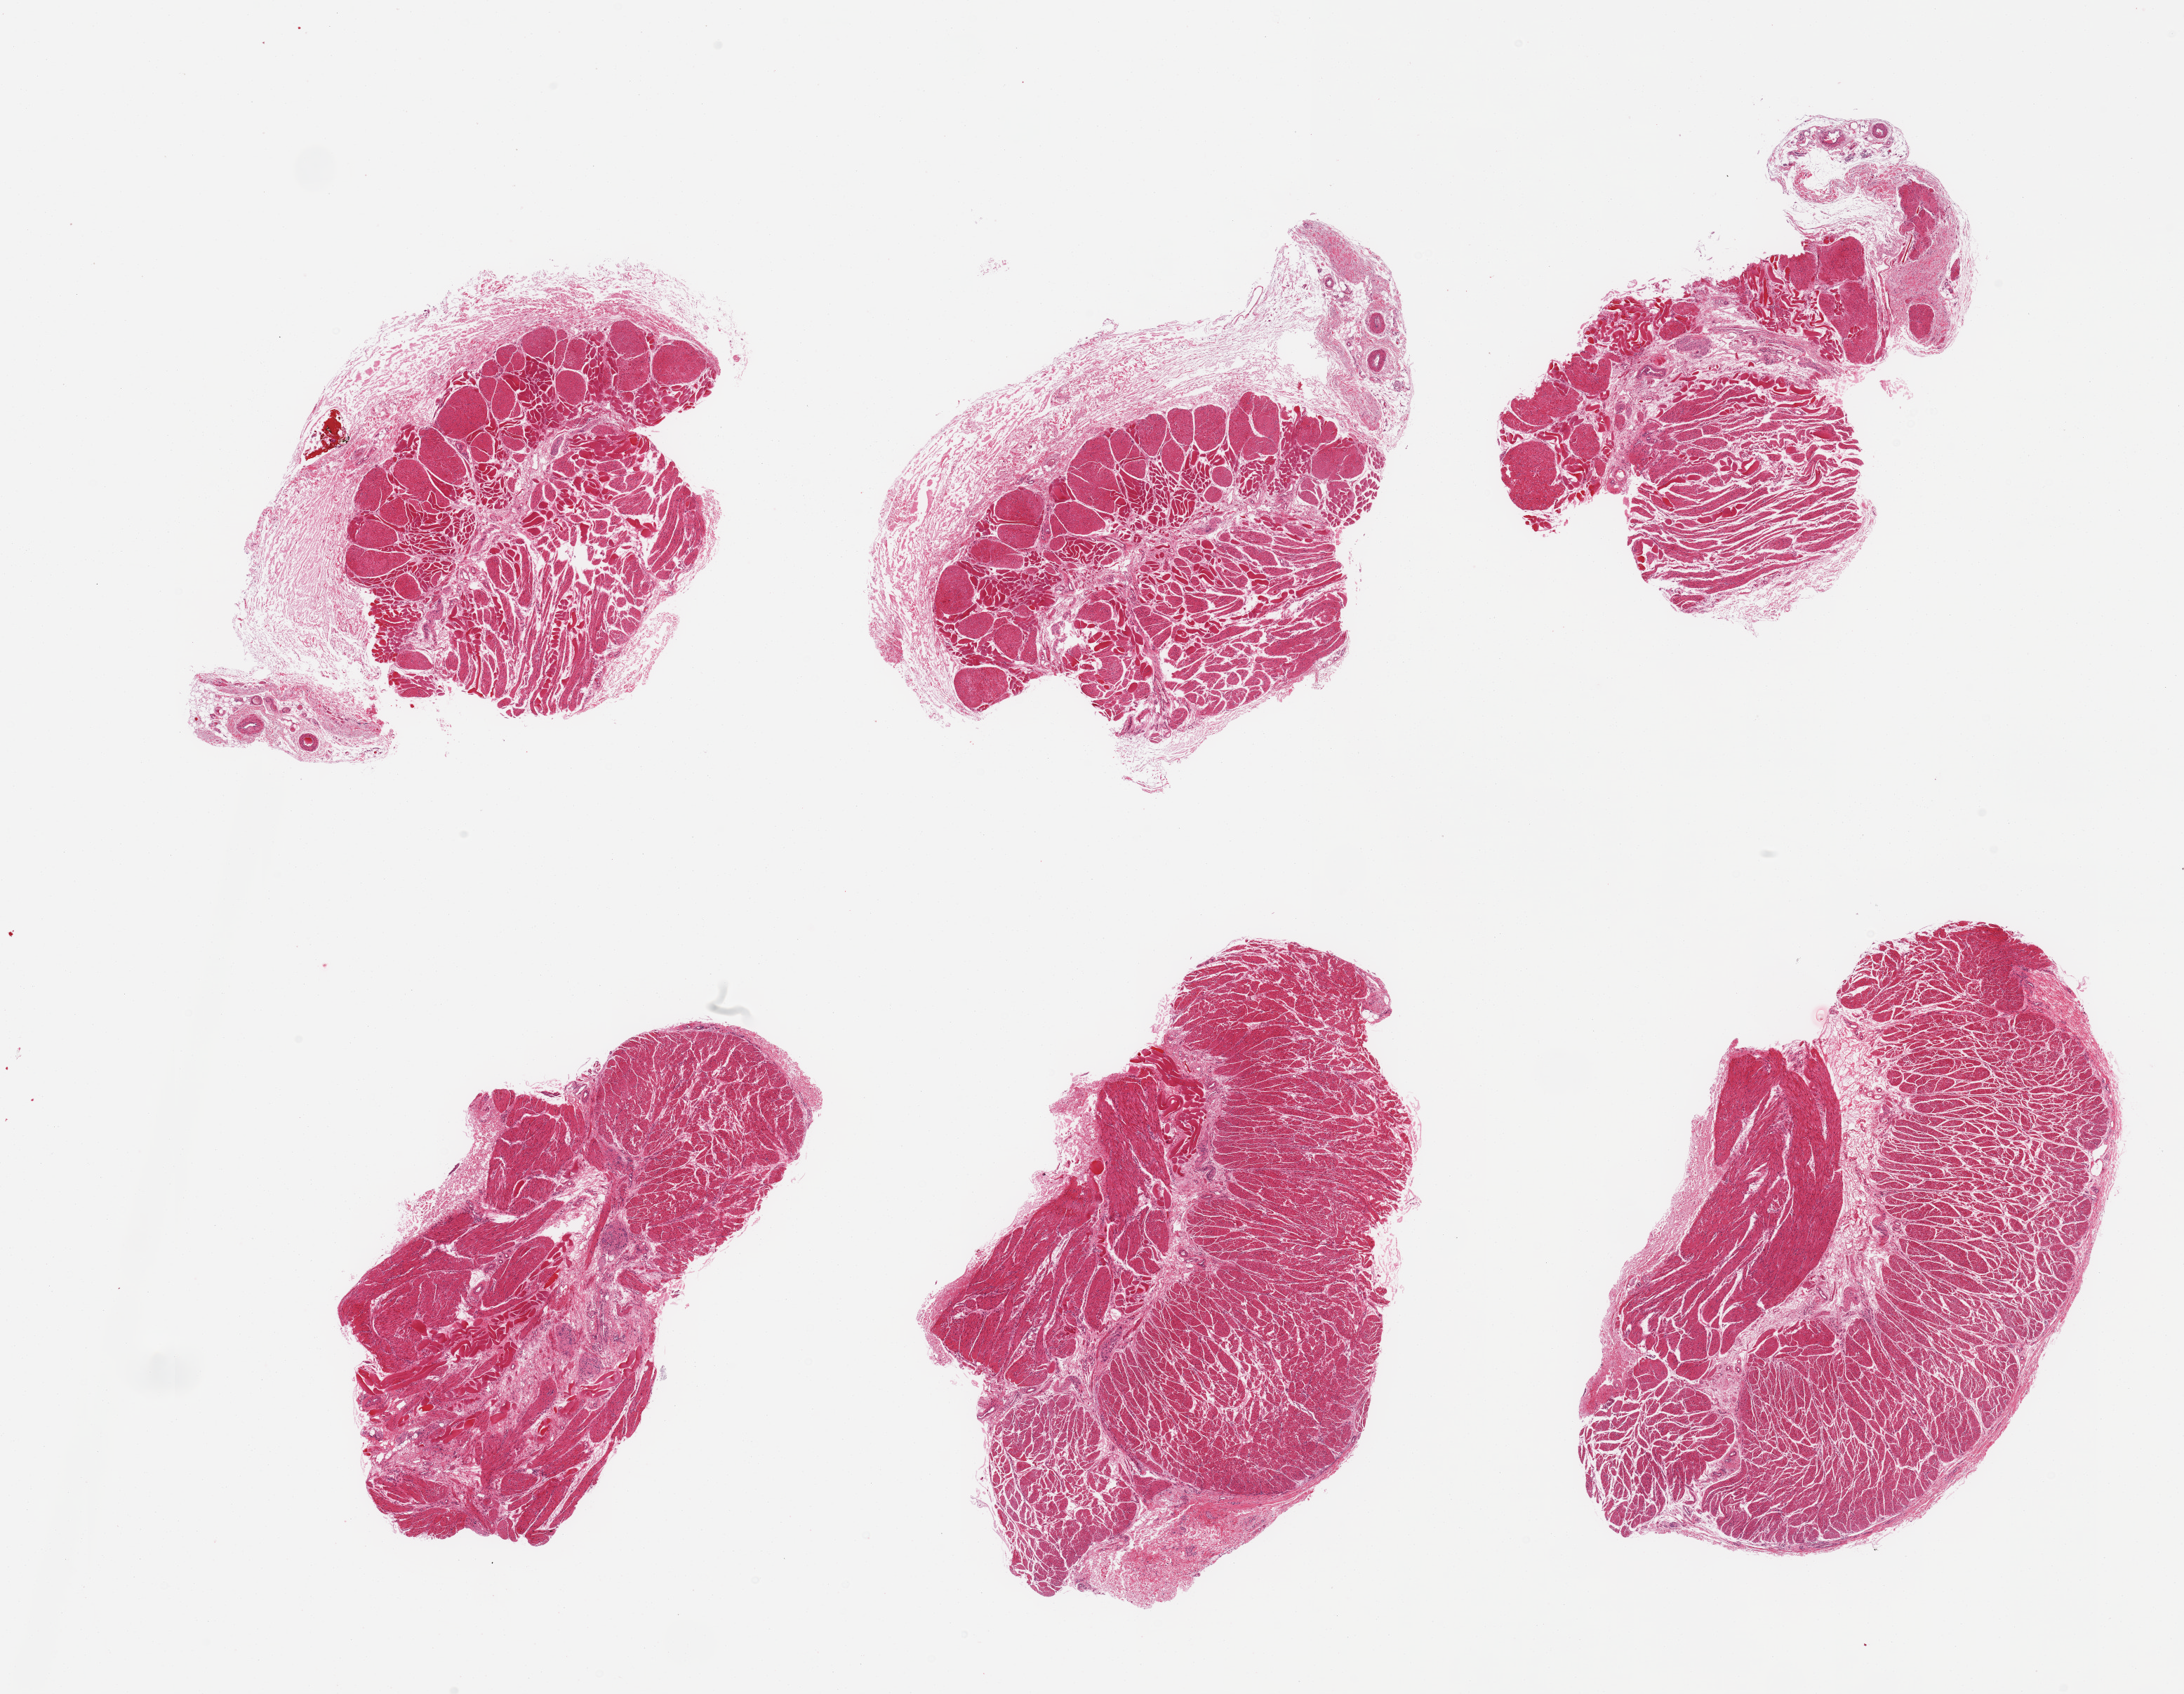
Digitized hematoxylin and eosin (H&E)-stained section — a low-resolution overview of the entire scanned area, about 24.6 x 19.1 mm (slide scanned at 20x); PAXgene-fixed paraffin-embedded (PFPE) section; section of esophageal muscle (target tissue); tissue donor sample.
Reviewer comment on this tissue sample: 6 pieces; target muscularis and up to 1.12mm attached moderately autolyzed serosa.